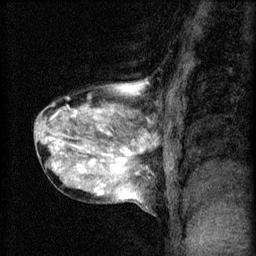
Breast MRI (dynamic contrast-enhanced), one sagittal slice; position 28 of 60 along the scan axis; 3 images stored at this slice position (order not interpretable as contrast timing); 1.5 T; TE 4.2 ms, TR 8.2 ms; 2 mm slice thickness; 256 × 256 image matrix, field of view 180 × 180 mm. Female patient, age 40 years.
Structures marked on this image (semi-automatically segmented with operator editing):
- analysis volume of interest (the breast-tissue region the enhancement analysis was run in; not a lesion): box from (x=33, y=80) to (x=167, y=211) px
- tumour enhancement mask (voxels above the 70 % enhancement threshold inside the analysis volume of interest): (x=47, y=88)–(x=148, y=195)